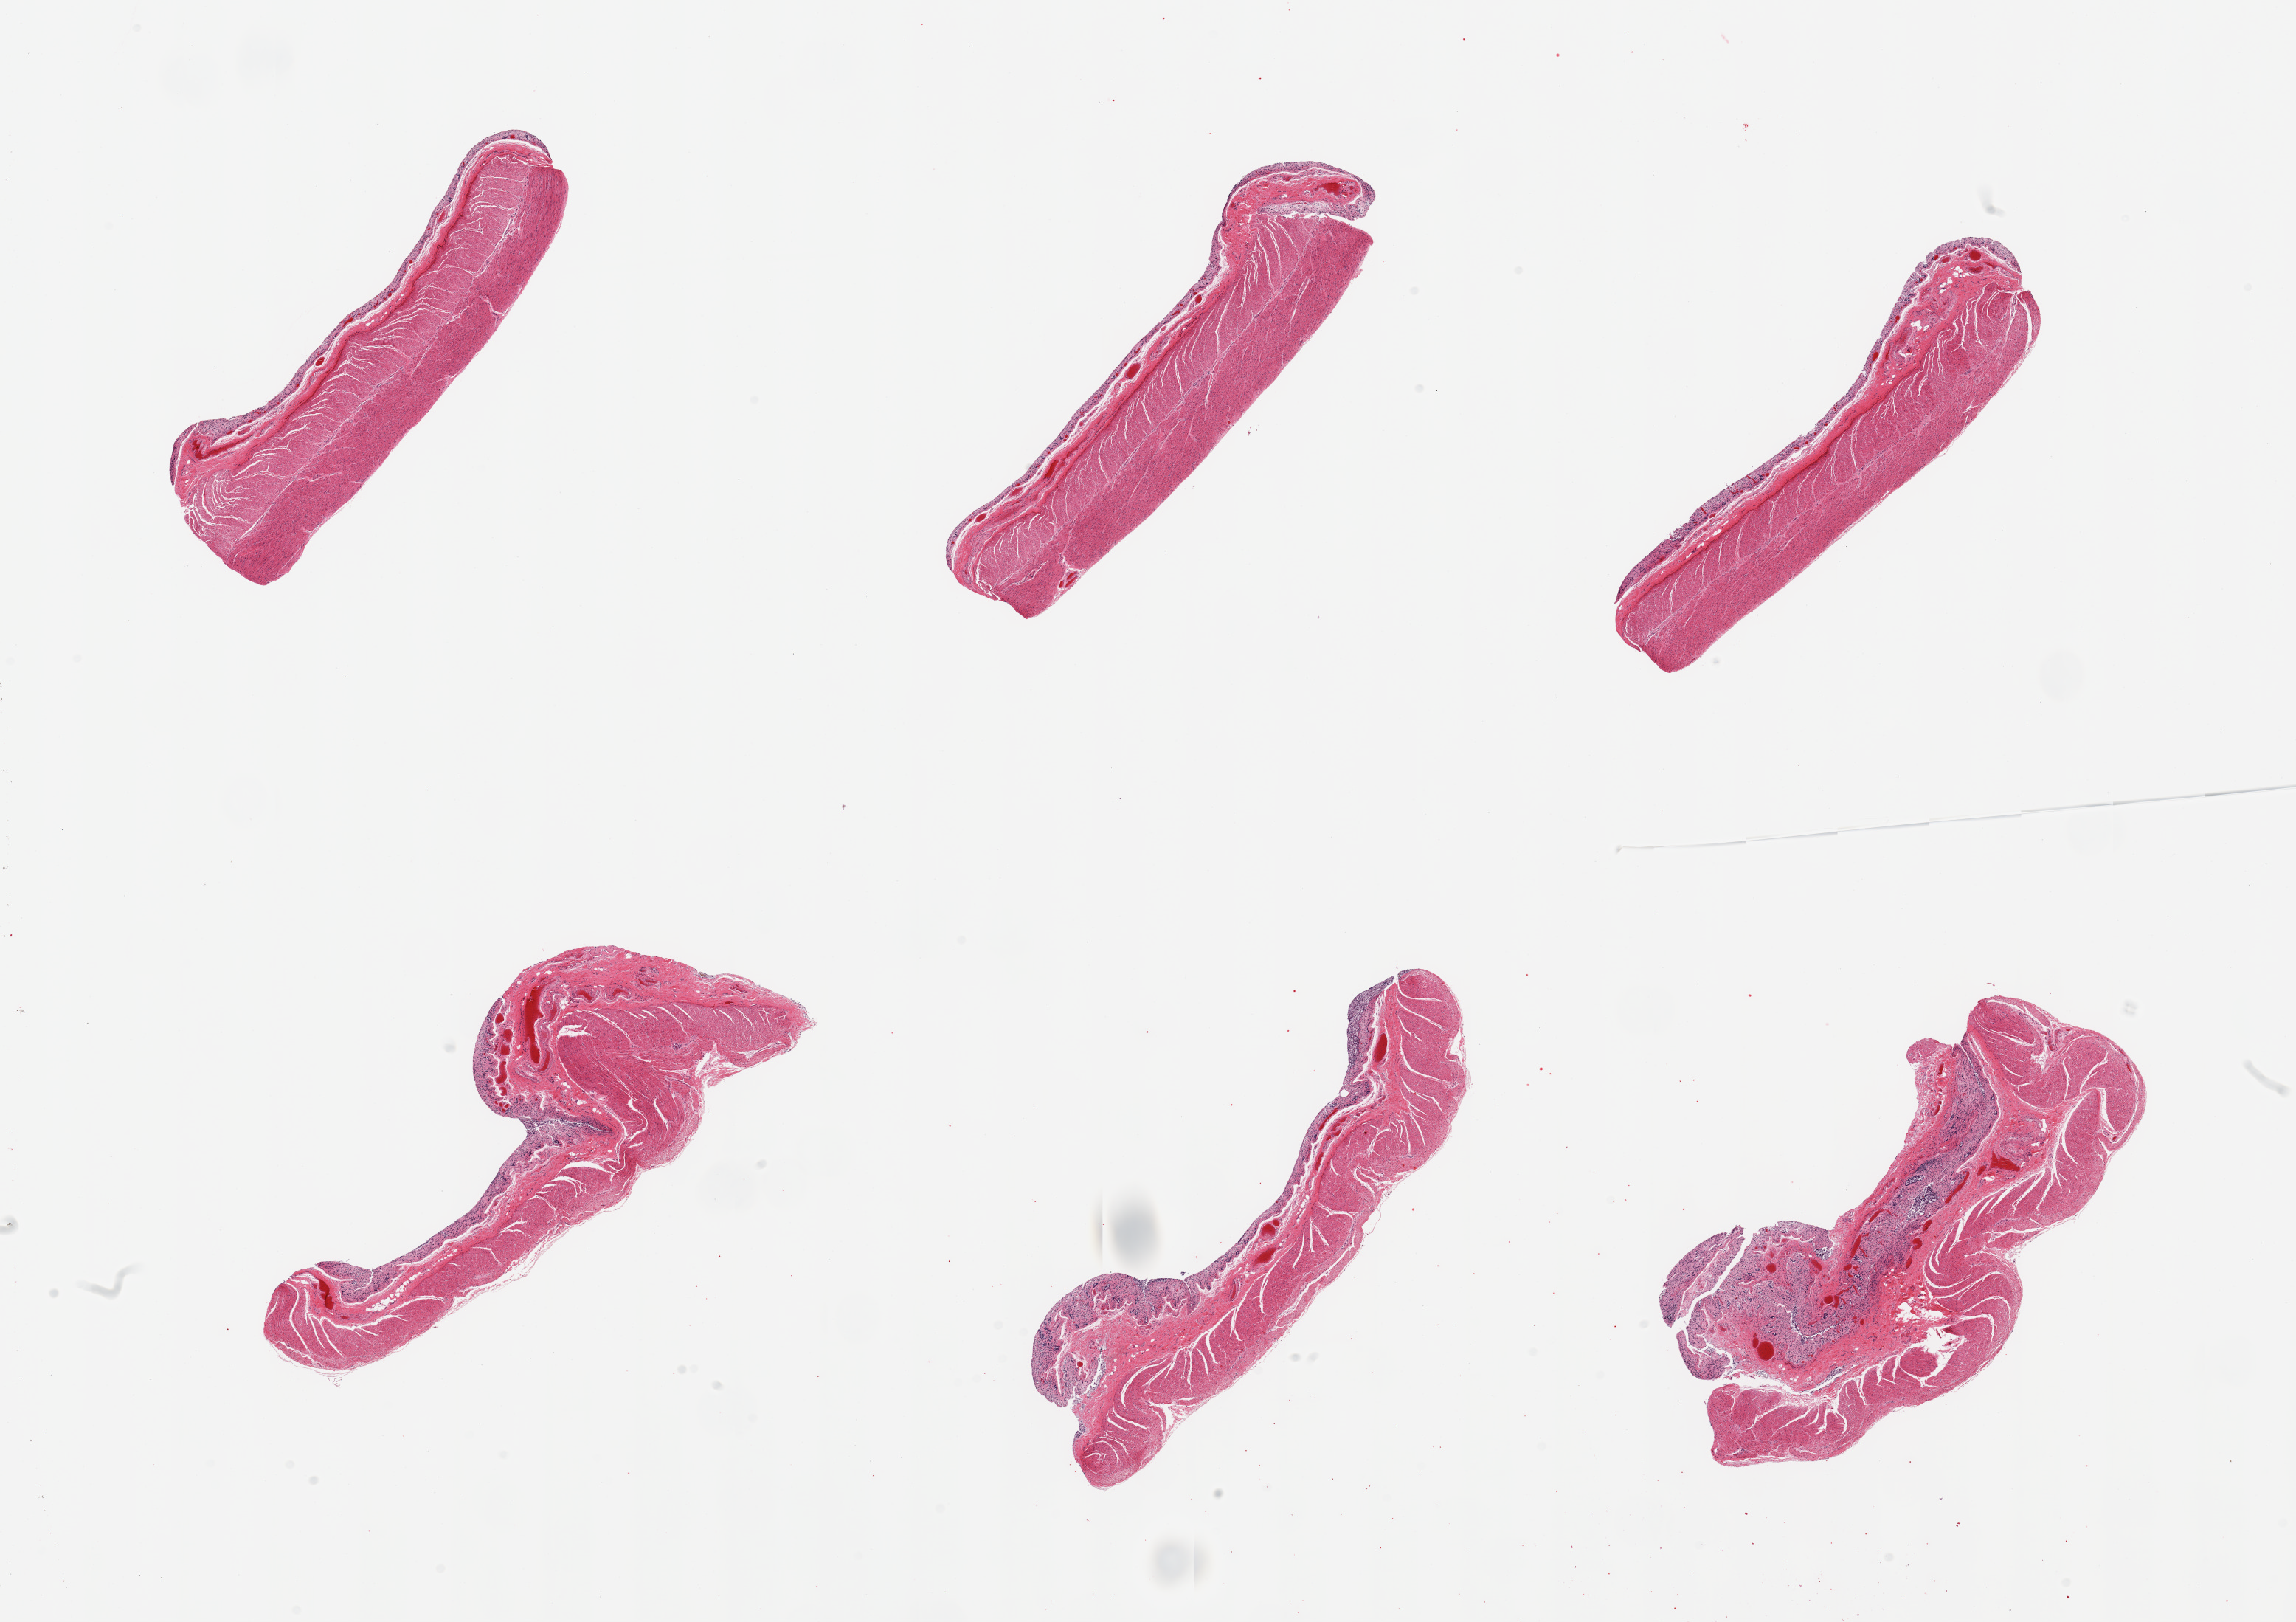
Digitized hematoxylin and eosin (H&E)-stained section — a low-resolution overview of the entire scanned area, about 24.6 x 17.4 mm; PAXgene-fixed paraffin-embedded (PFPE) section; target tissue: transverse colon; tissue donor sample. Male donor.
Pathologist's review note for this sample: 6 pieces; mucosa=3;muscle = 1 (autolysis).